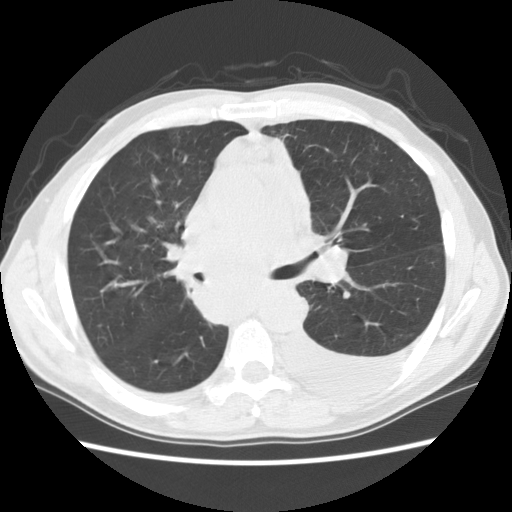
Axial slice from a low-dose chest CT screening exam. Baseline screening round. Lung window (W 1500 / L -600 HU). Male, age 60 years at enrolment.
- Lesion marked by an expert reader, bounding box (x1, y1, x2, y2) in pixels: (177, 238, 297, 329).
- No non-calcified nodule or mass ≥4 mm was recorded by the screening reader at this exam.